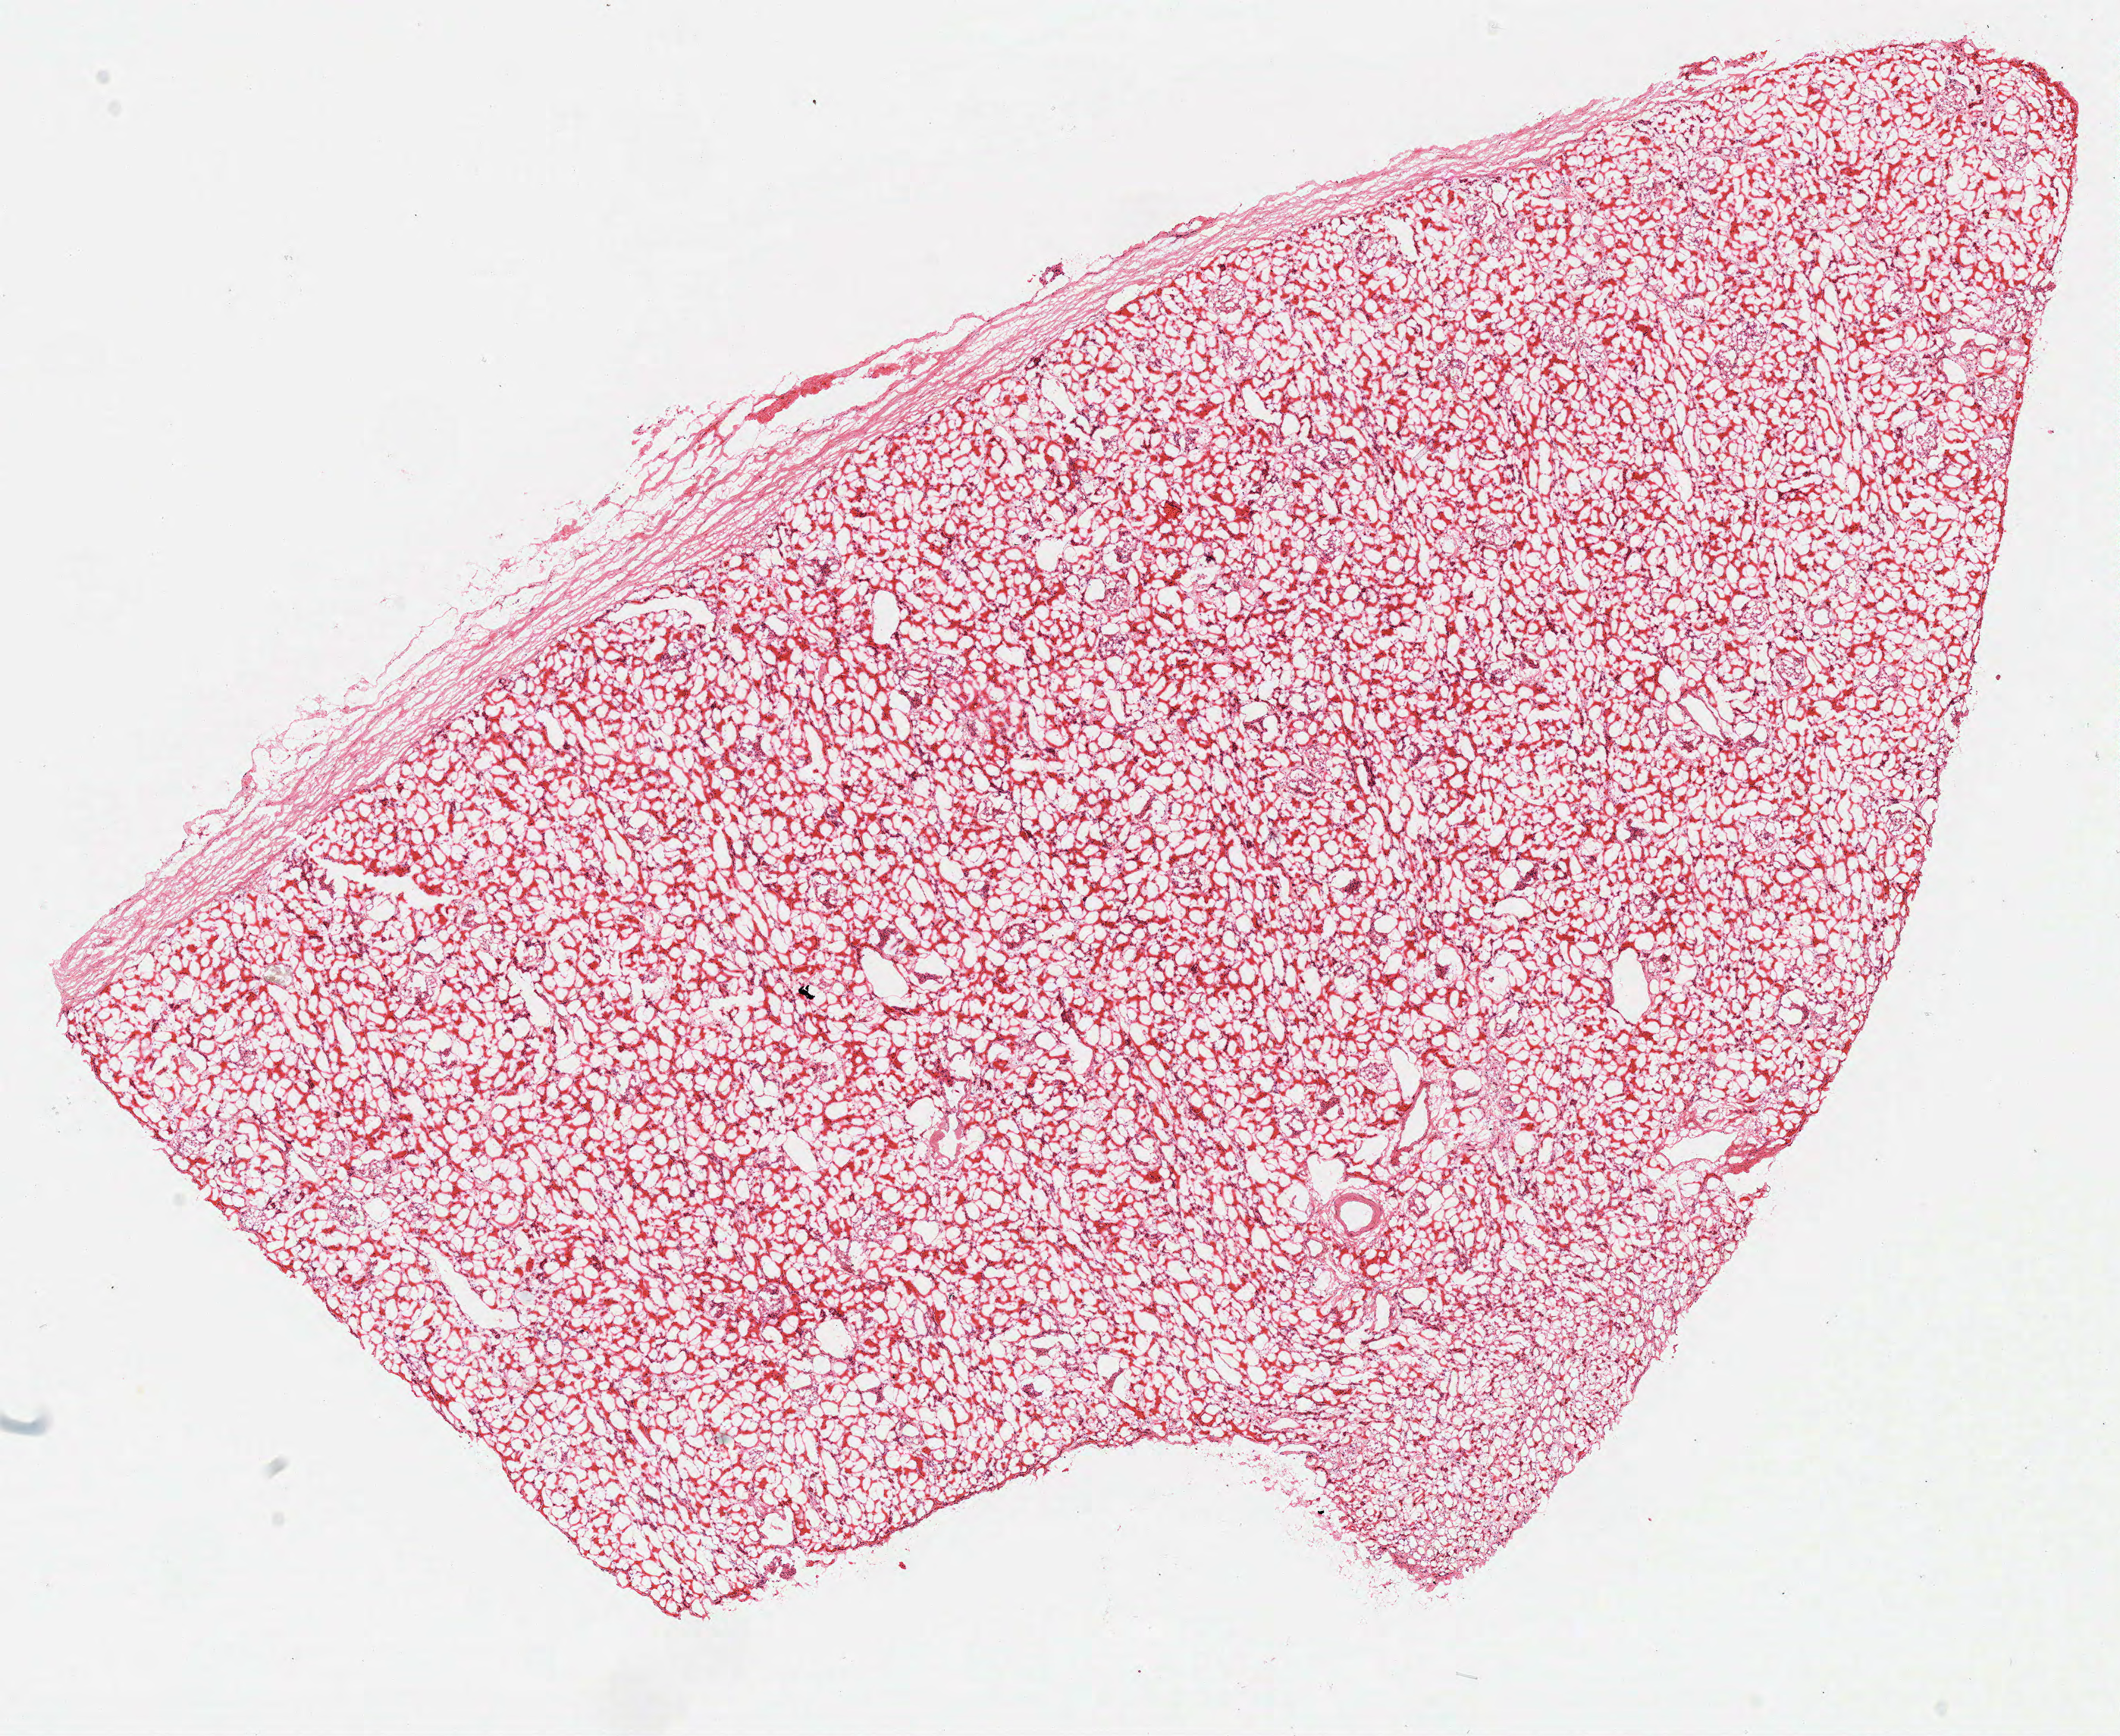
Digitized Hematoxylin and eosin (H&E) stained tissue section (whole slide) — shown as a low-resolution overview of the whole scanned area (about 11.0 x 9.0 mm, slide scanned at 40x), frozen section from the top of the tissue portion, sample: solid tissue normal (non-tumour tissue), kidney. Female patient; age at initial diagnosis 59 years.
This section: solid tissue normal (non-tumour) sample from the same patient. Patient diagnosis: Clear cell adenocarcinoma, NOS.